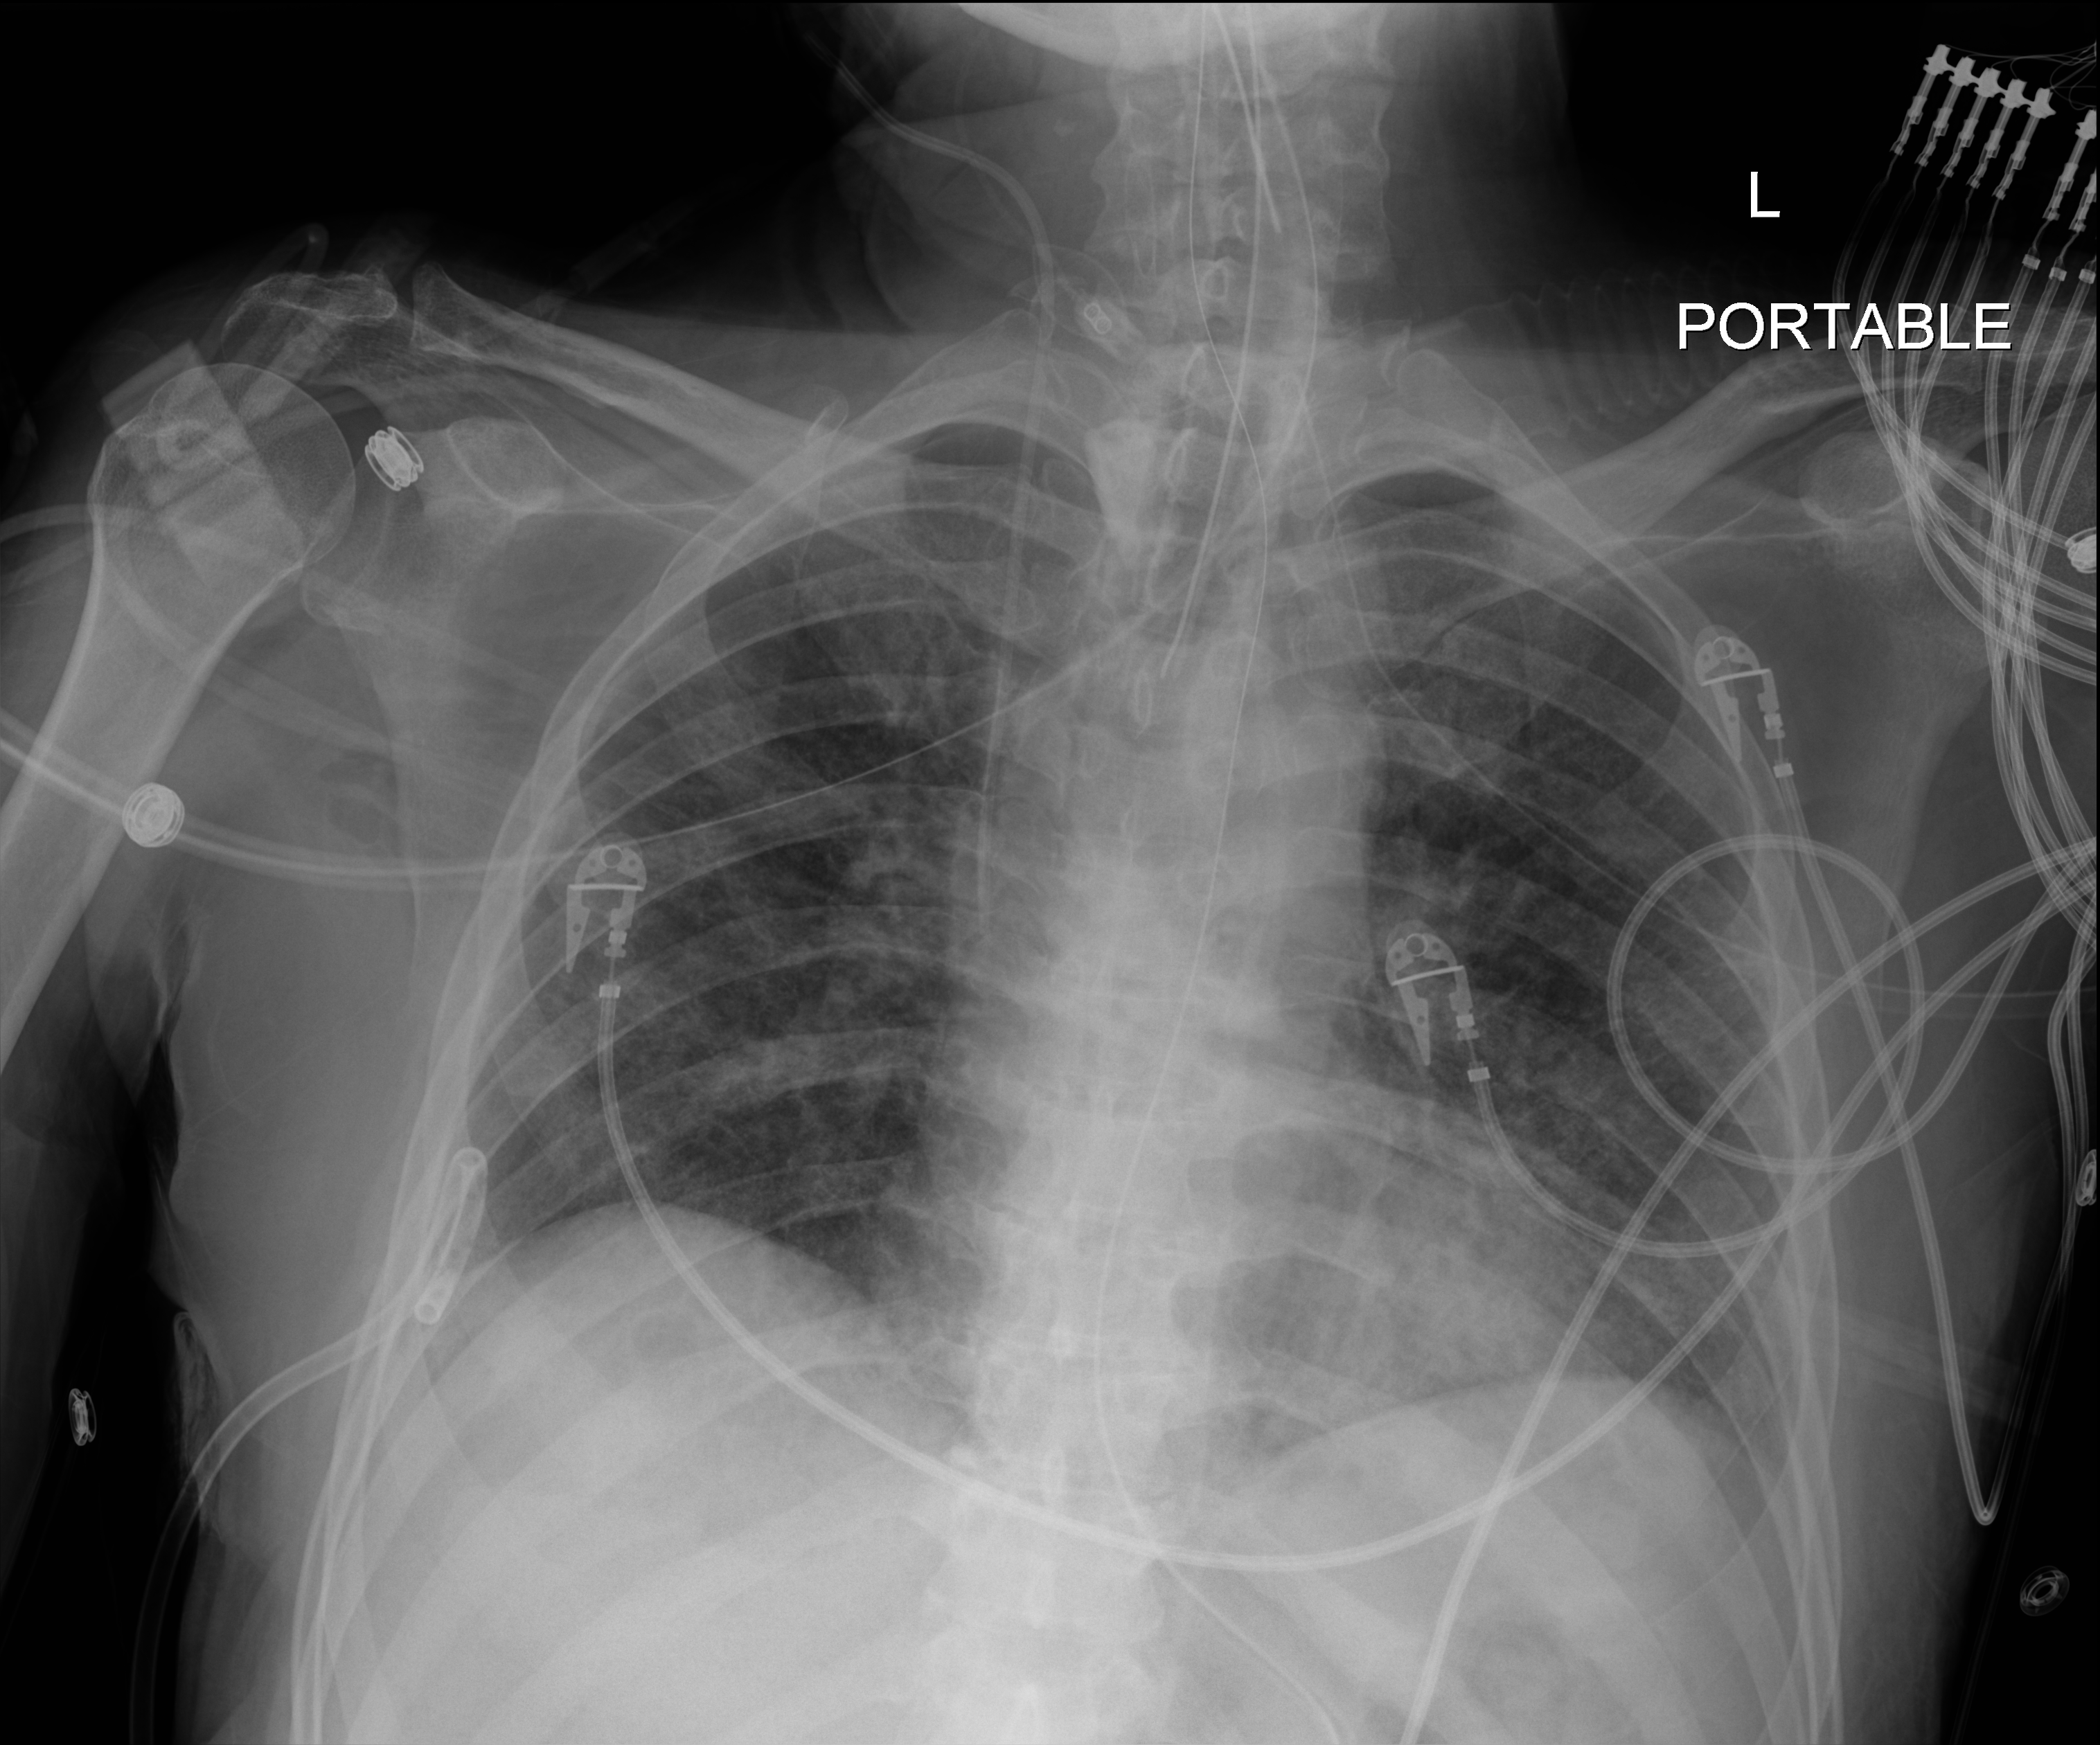
Bedside chest radiograph (digital radiography). Male patient hospitalised with COVID-19, age 18–59 years.
From the hospital-stay record, not from the radiograph (when in the stay this image was taken is not recorded): COPD (admission record): no; mechanically ventilated during this hospital stay: yes; other chronic lung disease (admission record): no.